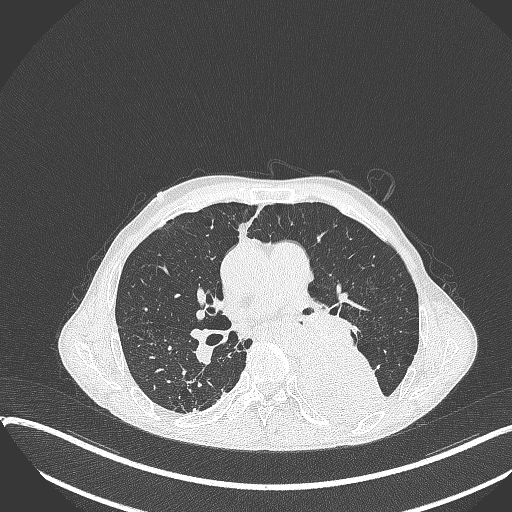
Chest CT, one axial slice. Position 206 of 401 along the scan axis. Reconstruction kernel B70f. Lung window (W 1500 / L -600 HU). 1 mm slice thickness. 512 × 512 image matrix, field of view 400 × 400 mm. Patient: male, 57 years. Case-level facts recorded for this patient, not image findings: clinical TNM (as recorded): T4 N0 M0.
Structures marked on this image (bounding box drawn by a radiologist):
- lung tumour (recorded histology: squamous cell carcinoma): bounding box [x1, y1, x2, y2] px = [291, 343, 386, 427]